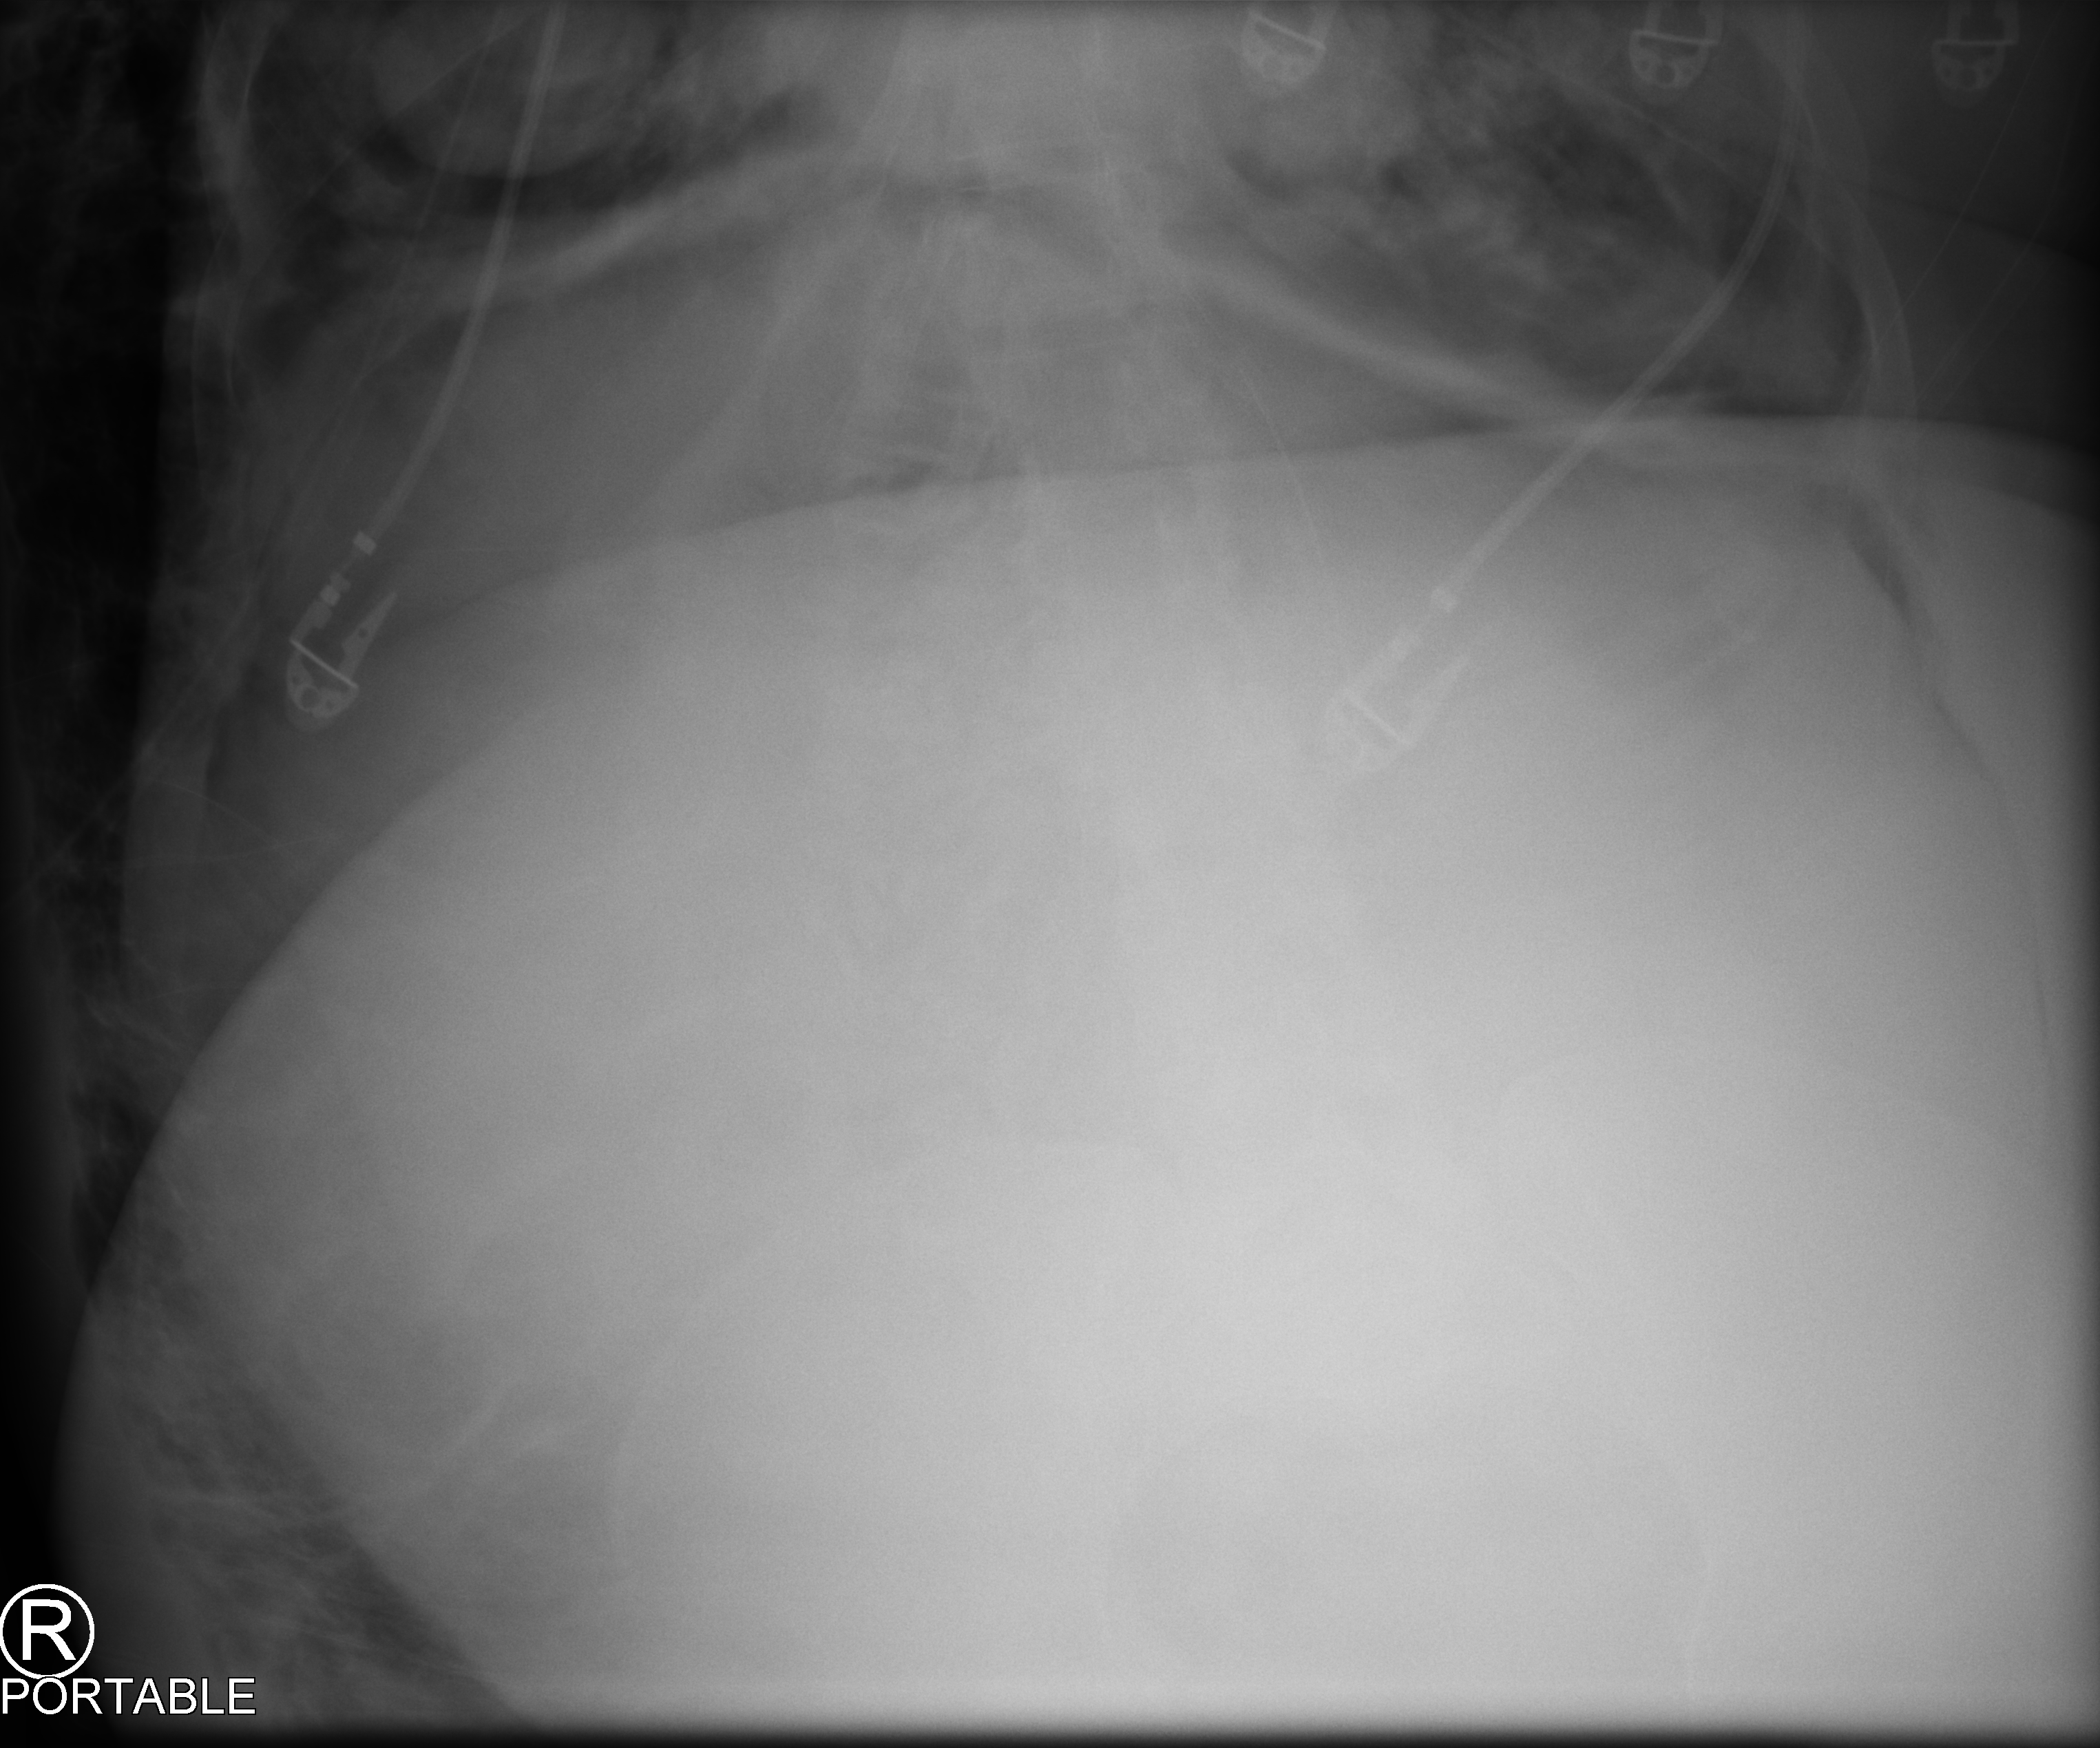
Bedside abdomen radiograph (computed radiography), anteroposterior (AP) projection. Patient hospitalised with COVID-19, aged 18–59 years.
Admission-level facts for this patient (not findings on this image; timing relative to this image not recorded): mechanically ventilated during this hospital stay: yes.